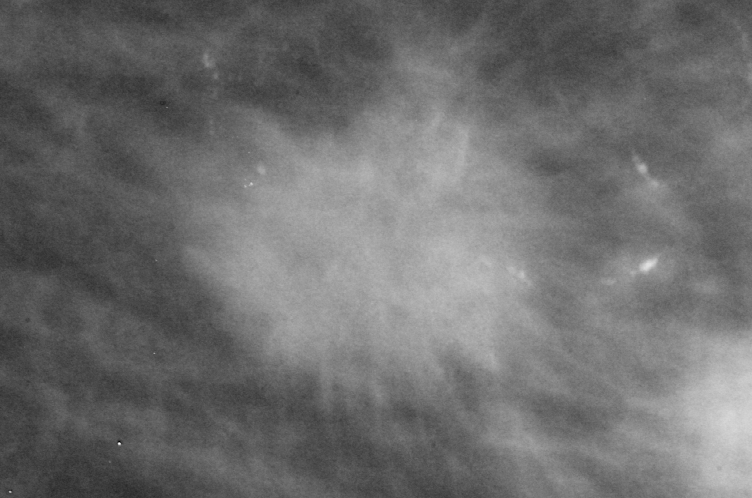
Region of interest cut from a scanned film mammogram (one marked finding), left breast, MLO view.
Finding: mass, shape irregular, margins spiculated; BI-RADS assessment category 5; subtlety rating 5 on a 1 (subtle) to 5 (obvious) scale; pathology result (as recorded, not read from the image): malignant.